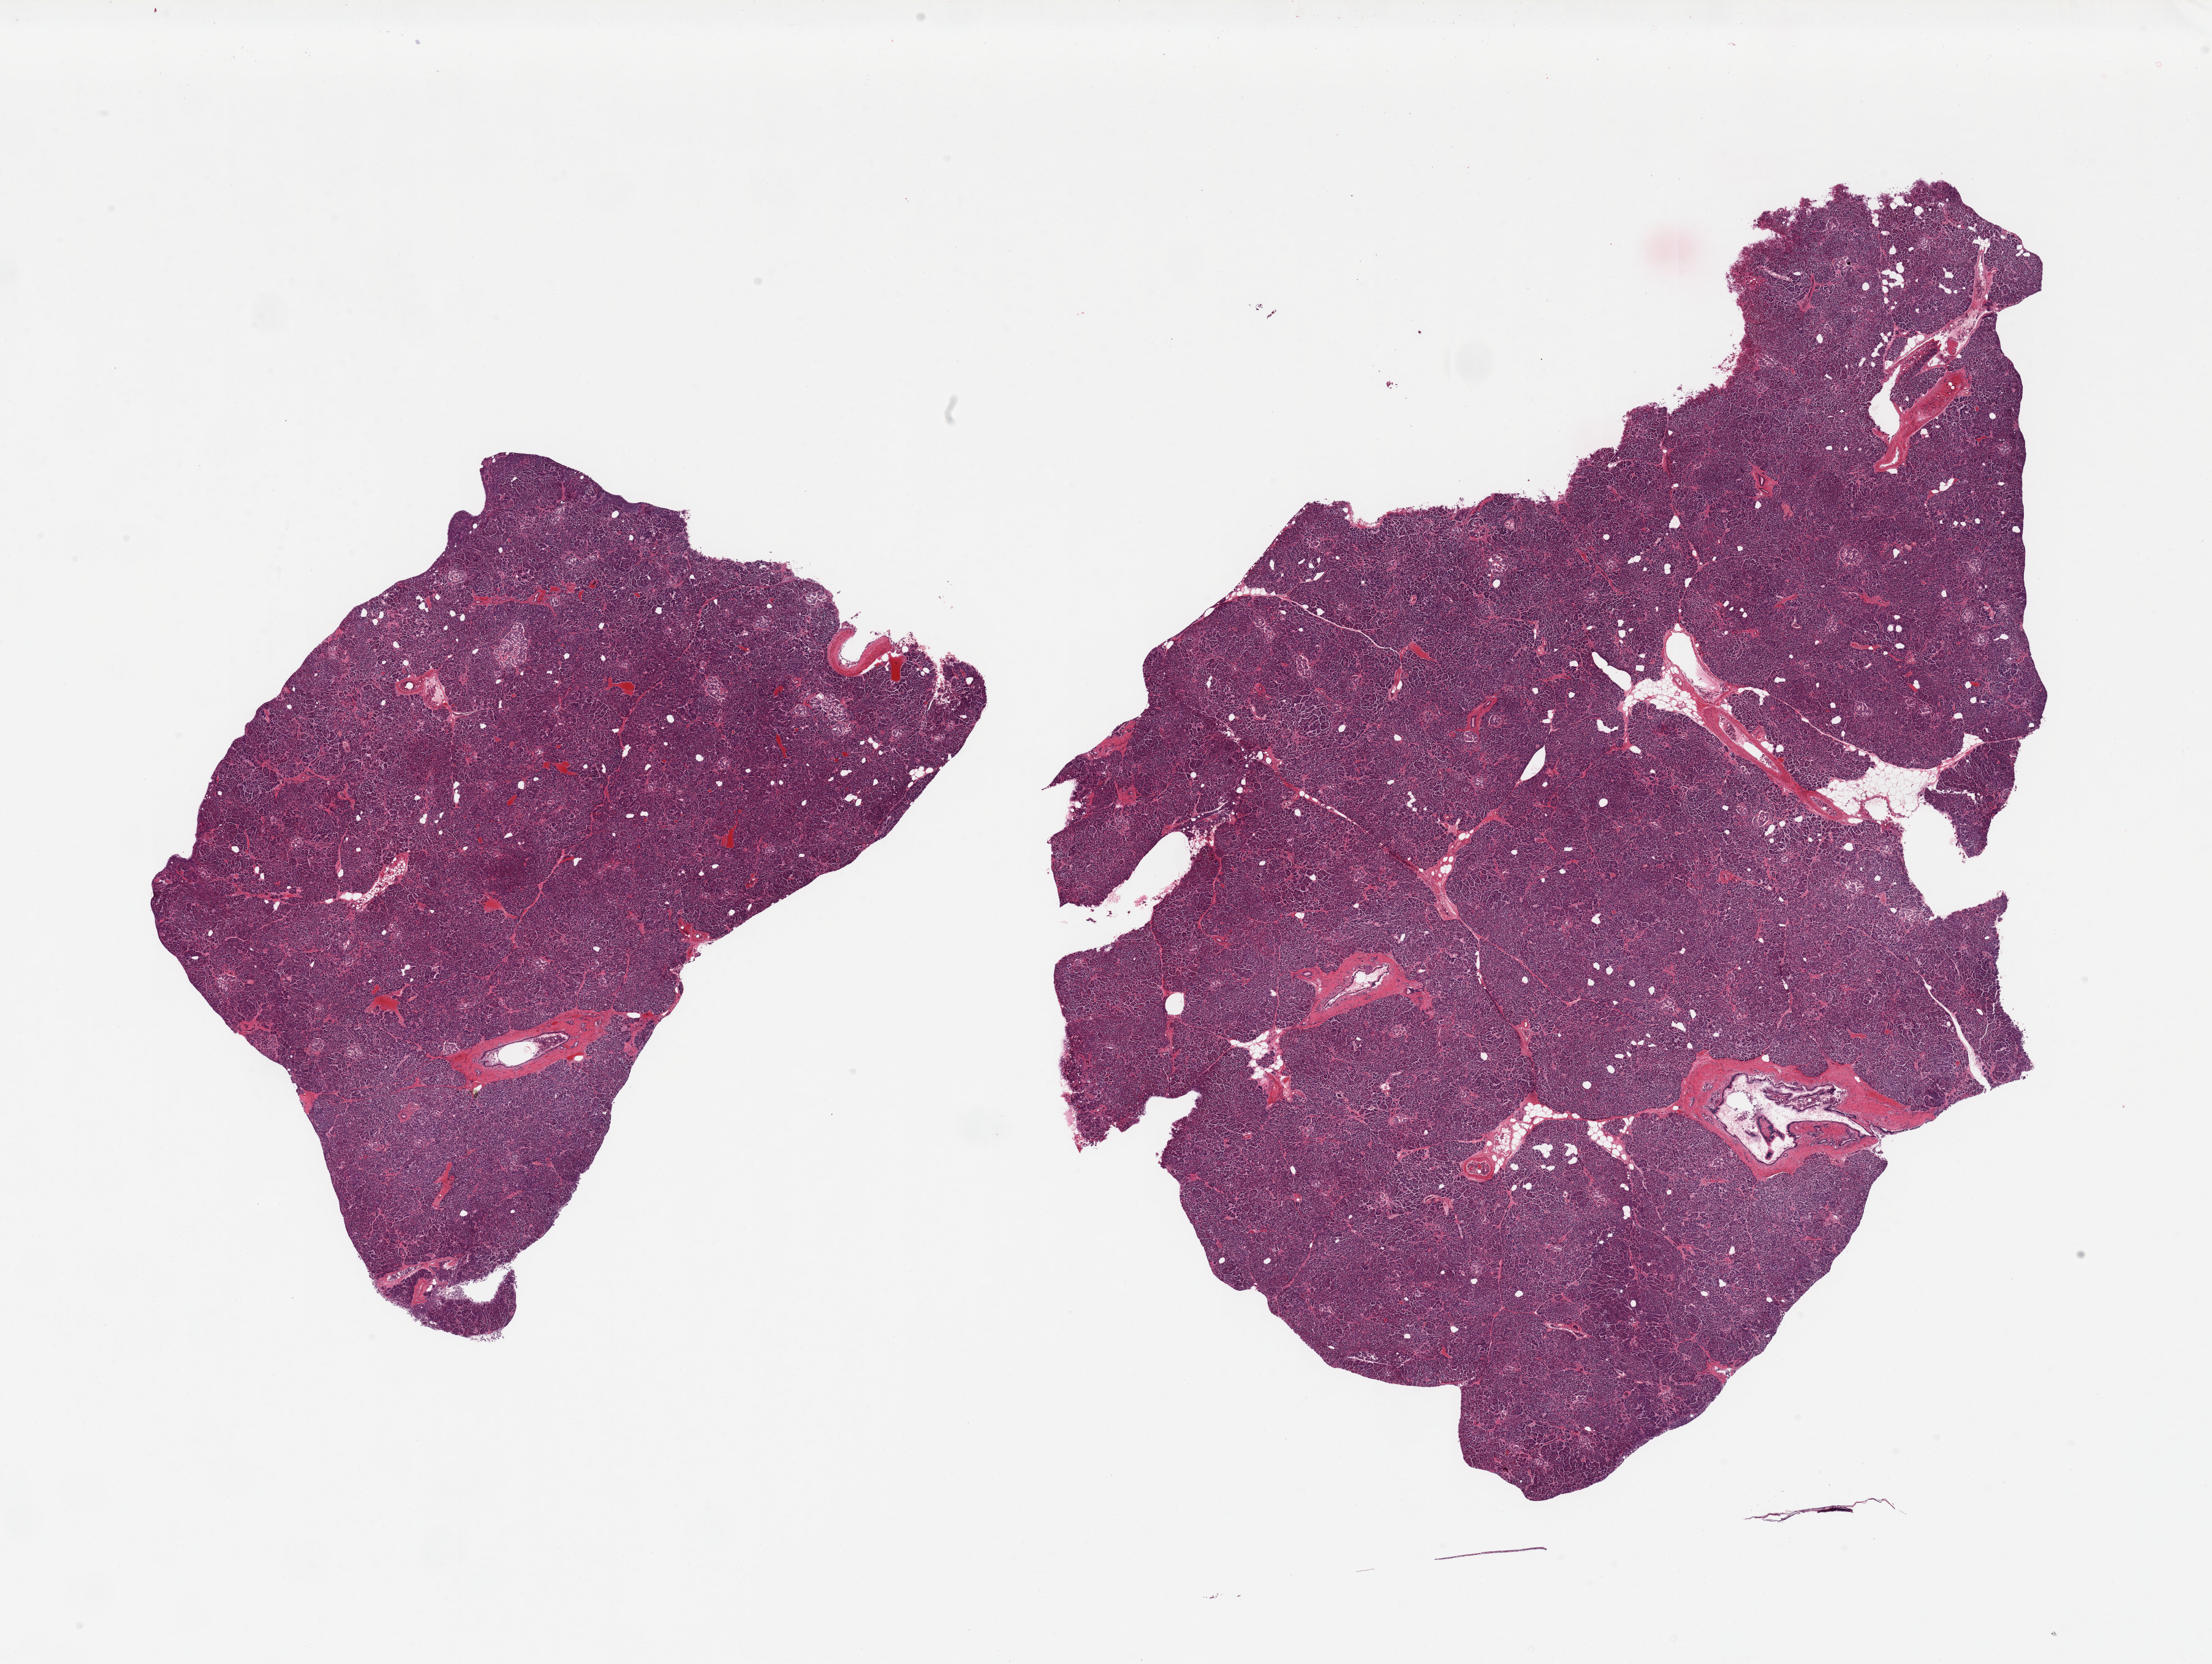
Digitized H&E-stained section, brightfield, whole scanned area (about 28.5 x 21.5 mm, from a 20x scan) shown as a low-resolution overview, PAXgene-fixed paraffin-embedded (PFPE) section, sampled site (target tissue): pancreas, tissue donor sample. Donor sex: male.
- pathologist's review note for this sample: 2 pieces; mildly periductal fibrosis; PanIN 1A changes in ducts